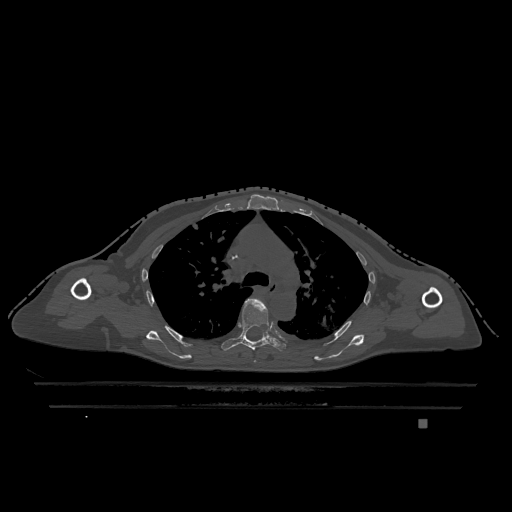
CT including the spine, one axial slice. Position 844 of 1317 along the scan axis. Bone window (W 1800 / L 400 HU). 0.5 mm slice thickness. 512 × 512 image matrix, field of view 500 × 500 mm. Patient: female, 74 years. Case-level facts recorded for this patient, not image findings: primary cancer: lung; vertebrae with lytic lesions (as recorded): T1, T4, T5, T6, L4, L5.
Annotated regions visible in this slice (semi-automatically segmented with operator editing):
- T5 vertebra: box from (x=221, y=298) to (x=286, y=353) px